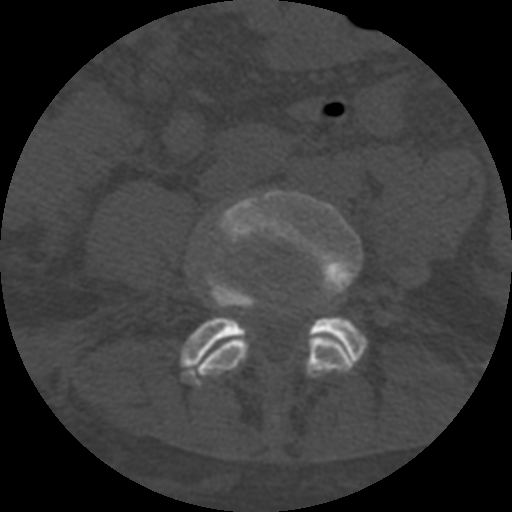
CT including the spine, one axial slice. Slice 197 of 708 in the series (ordered by position). Reconstruction kernel STANDARD. One of 3 acquisitions stored at this slice position. Bone window (W 1800 / L 400 HU). 1.25 mm slice thickness. 512 × 512 image matrix. Patient age 55 years. Case-level facts recorded for this patient, not image findings: primary cancer: colon; vertebrae with lytic lesions (as recorded): T12, L1, L5.
Structures marked on this image (semi-automatic segmentation, software-assisted and operator-edited):
- L4 vertebra: bounding box [x1, y1, x2, y2] px = [199, 190, 363, 378]
- L5 vertebra: [181, 272, 367, 385]